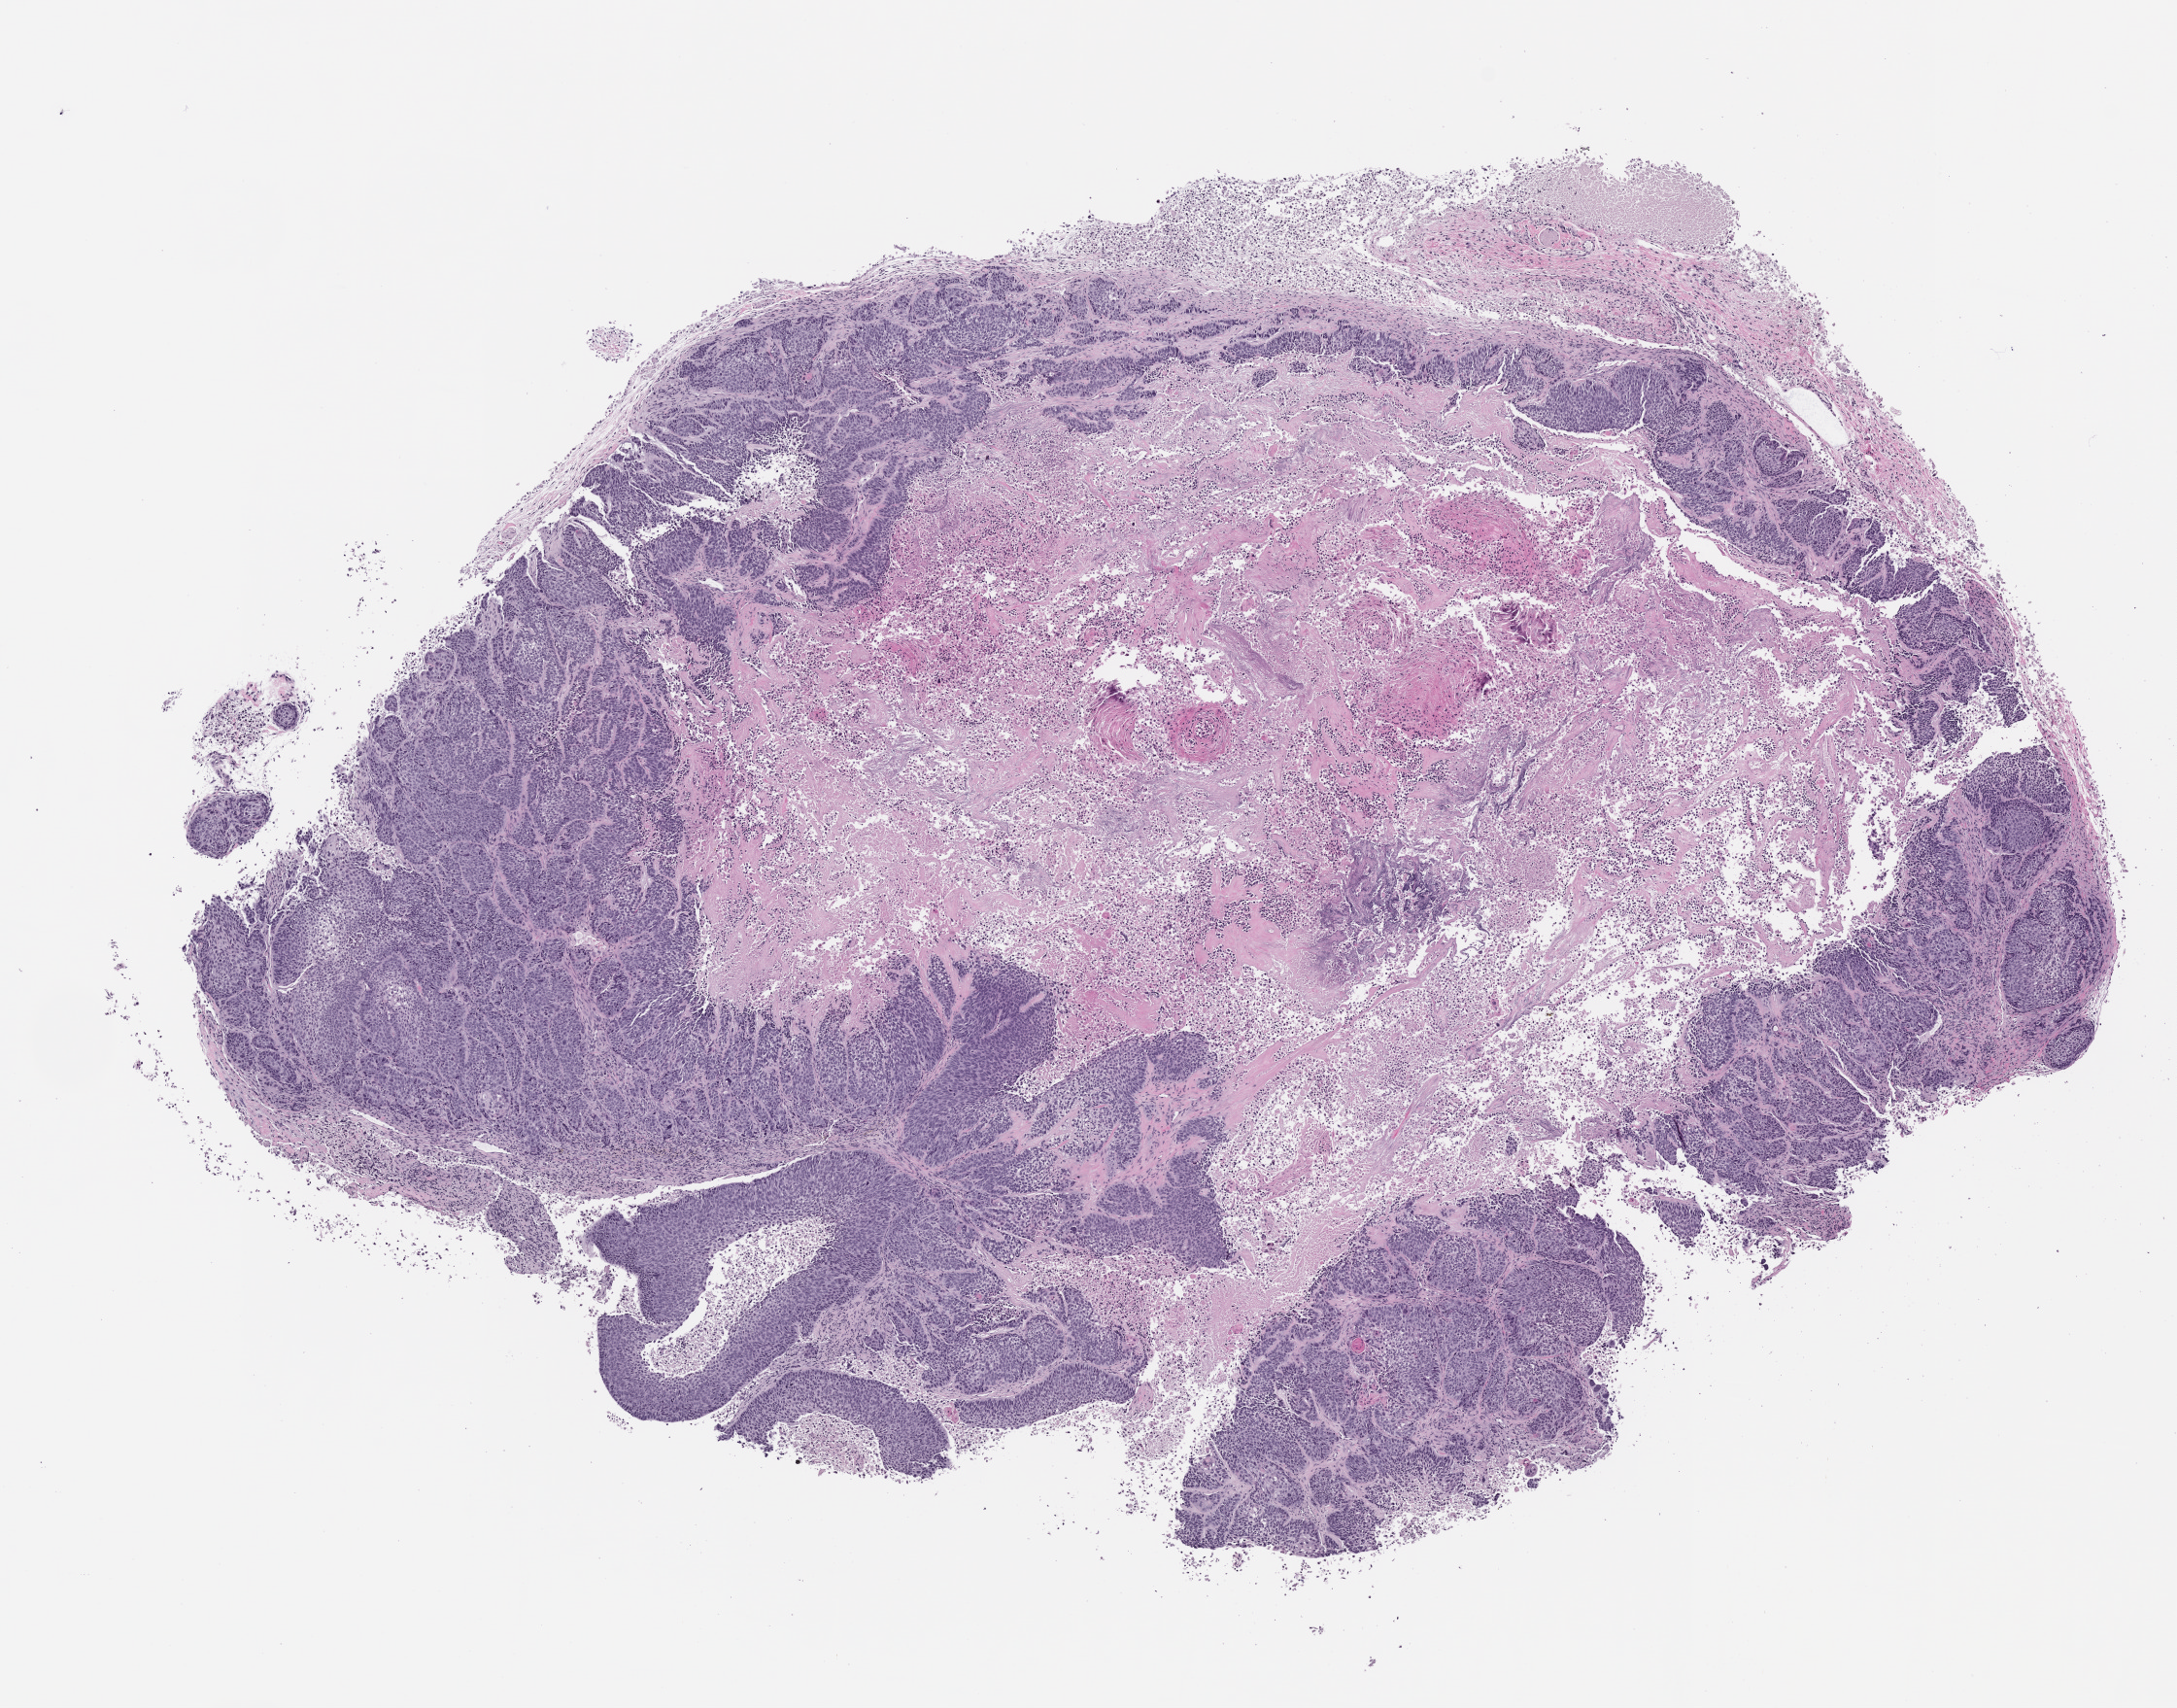
Whole-slide image, hematoxylin and eosin (H&E): patient-derived xenograft (human tumor grown in a mouse) — shown as a low-resolution overview of the whole scanned area (about 9.0 x 7.1 mm). Formalin-fixed paraffin-embedded section. Originating tumor site category: lung.
* originating patient diagnosis: Lung Squamous Cell Carcinoma